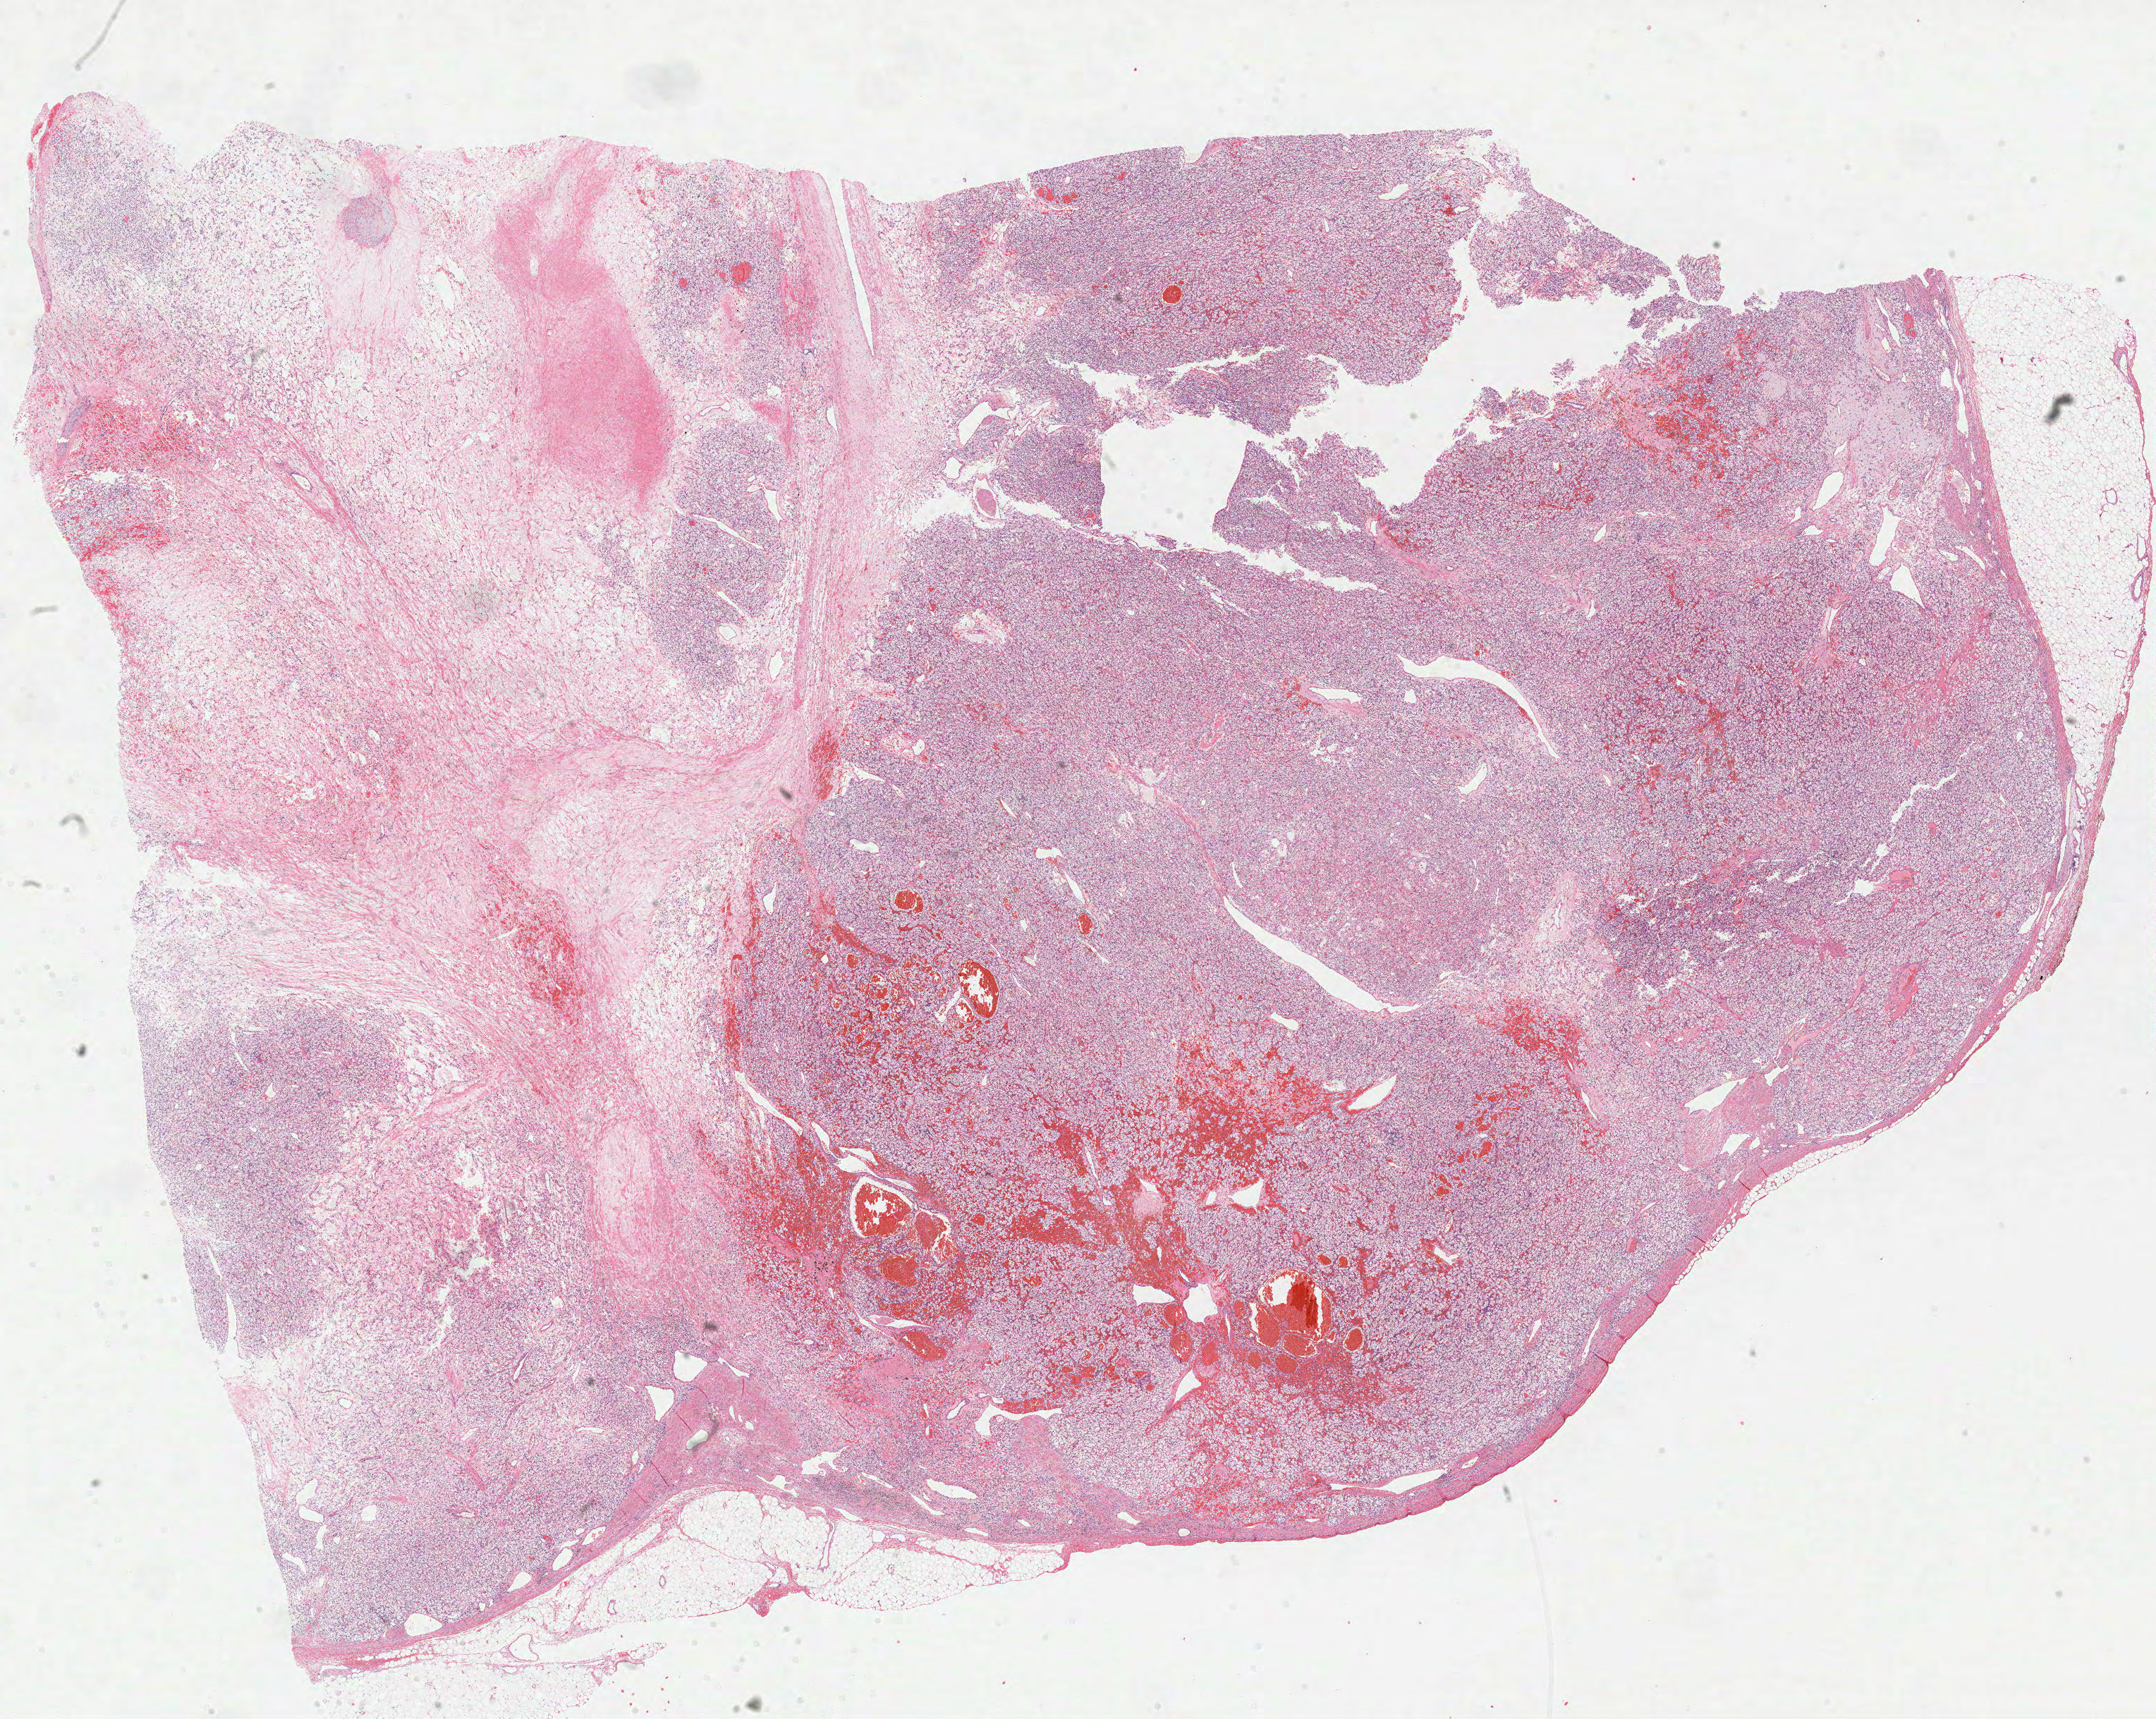
H&E-stained whole-slide image — shown as a low-resolution overview of the whole scanned area (about 24.7 x 19.7 mm, slide scanned at 40x). Formalin-fixed paraffin-embedded (FFPE) diagnostic section. Kidney, primary tumour sample. Patient: male, age at initial diagnosis 55 years. Histologic grade: G2 (moderately differentiated).
* diagnosis: Clear cell adenocarcinoma, NOS
* TNM: T1b NX M0
* AJCC pathologic stage: I (7th edition)